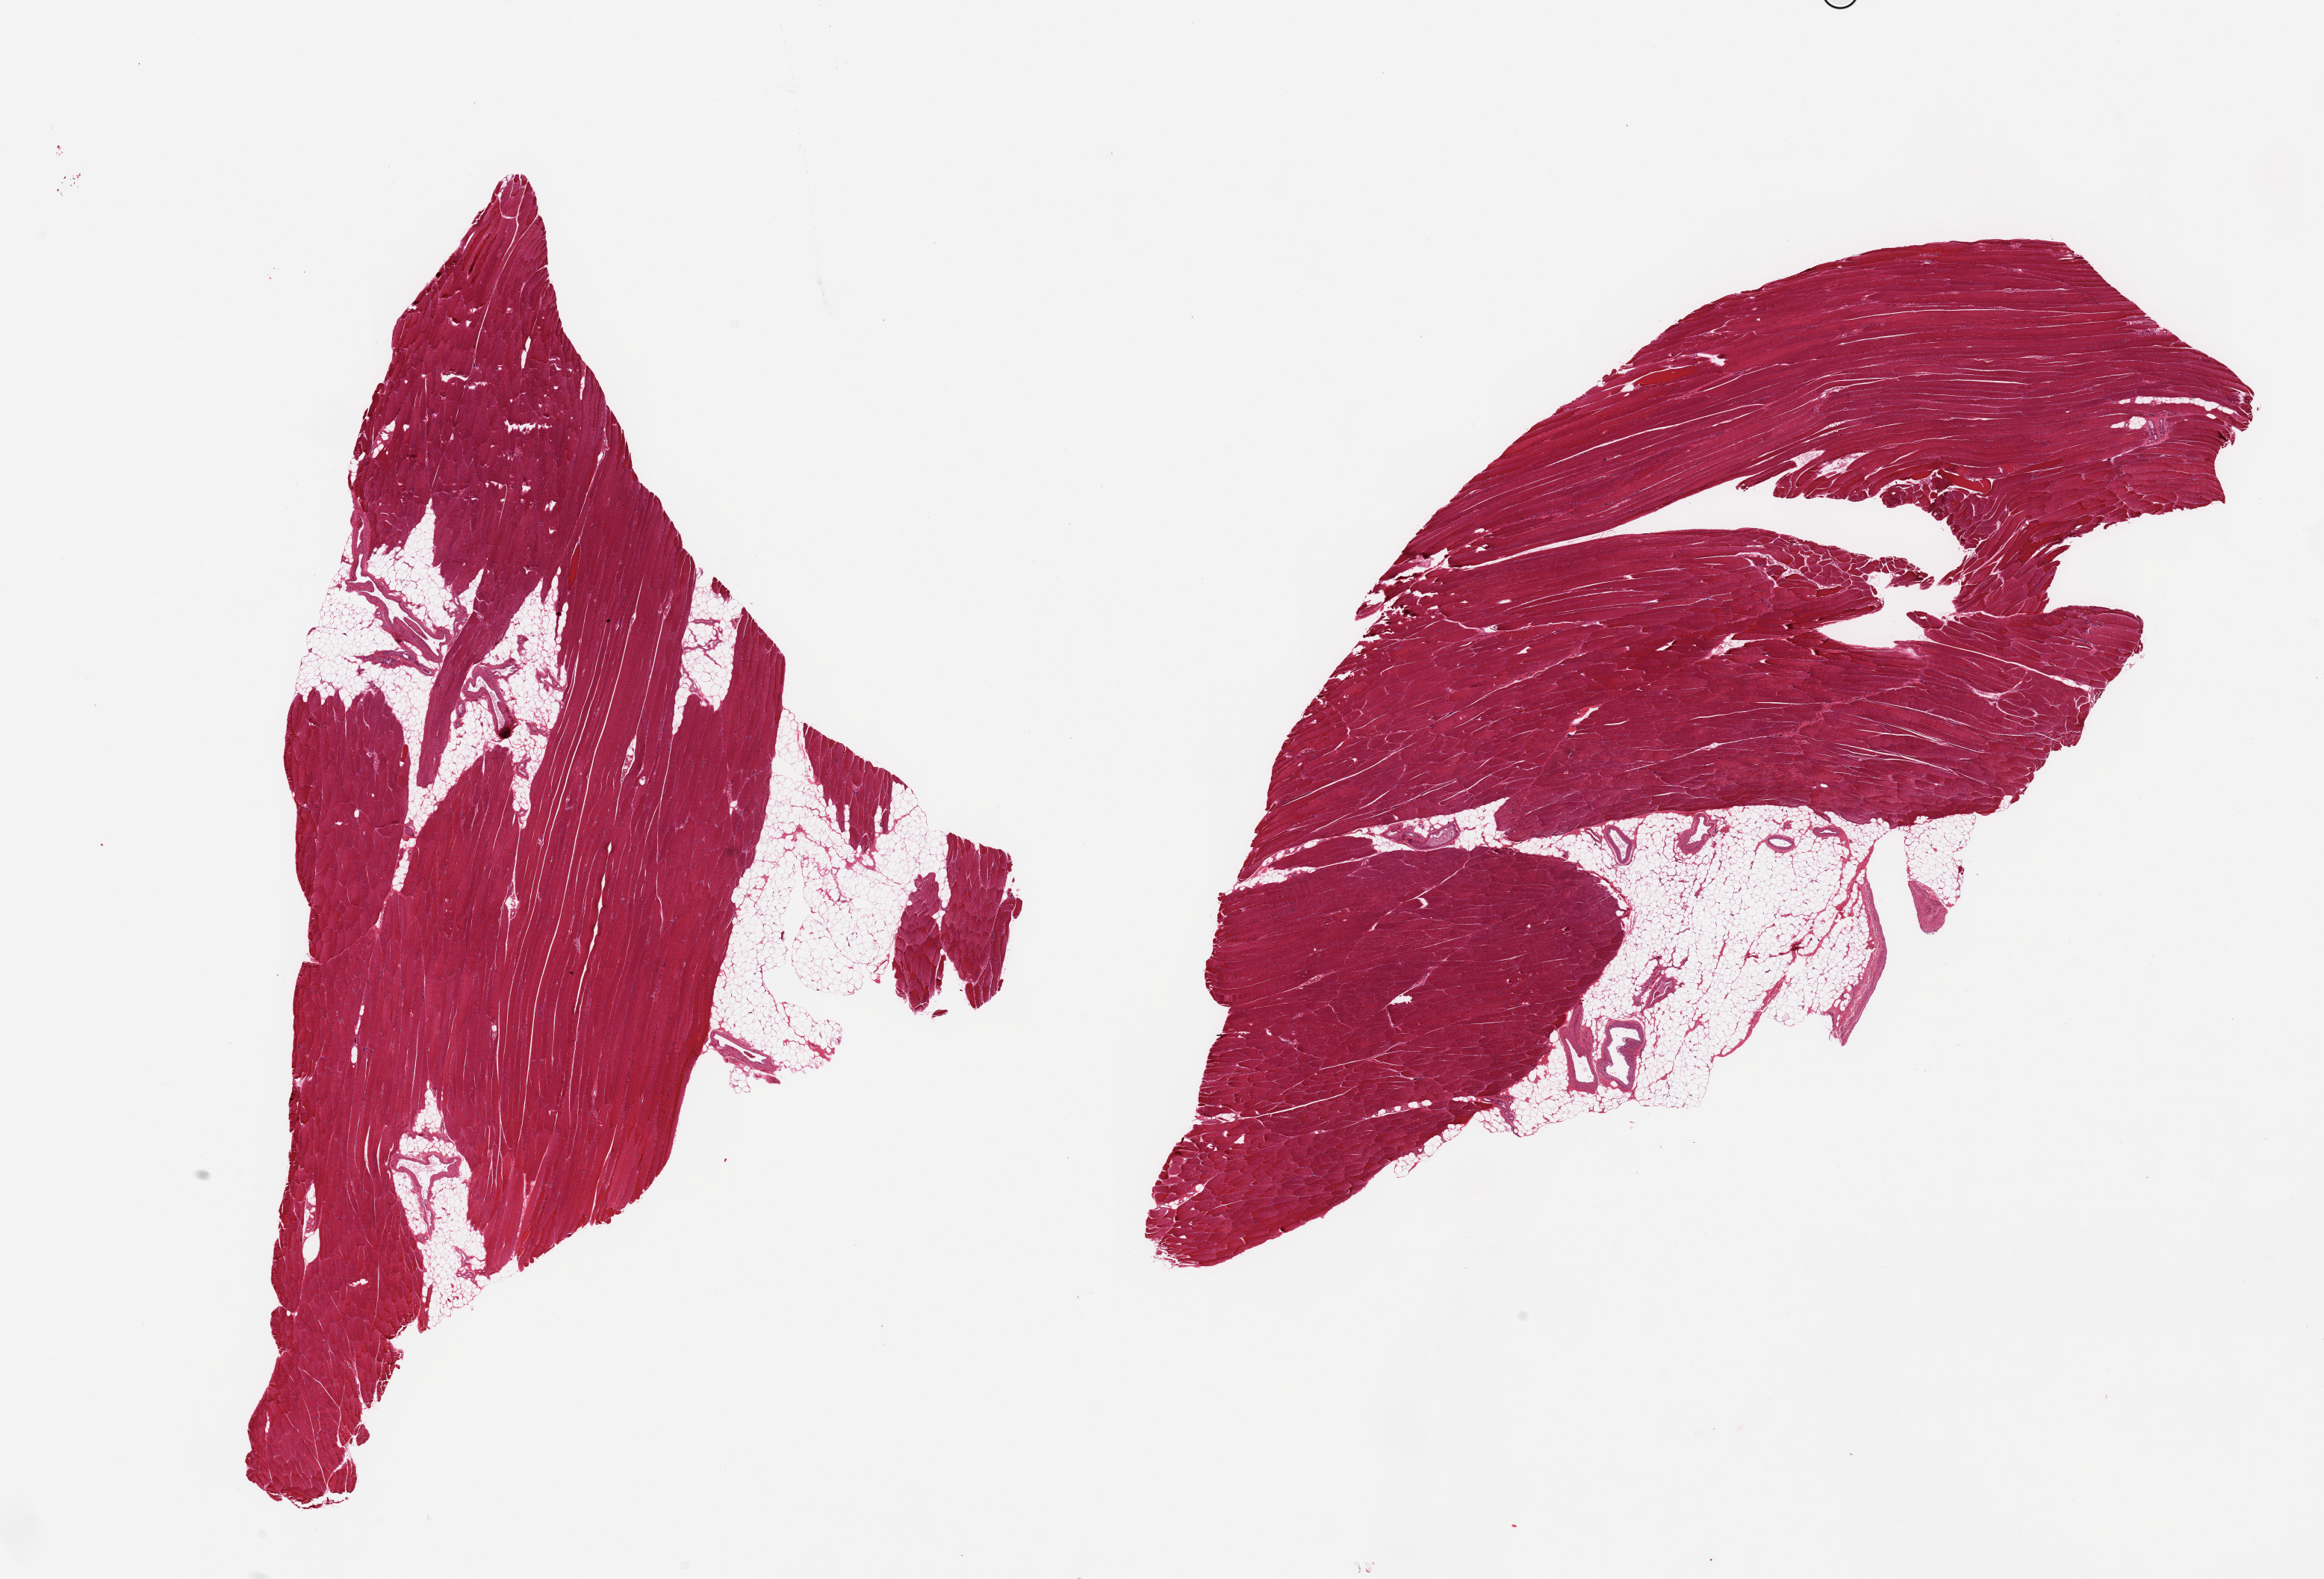
Haematoxylin and eosin whole-slide image, shown as a low-resolution overview of the whole scanned area (about 24.6 x 16.7 mm), PAXgene-fixed paraffin-embedded (PFPE) section, target tissue: skeletal muscle, donor tissue sample. Male donor.
- pathologist's review note for this sample: 2 pieces; 20% internal and external fat